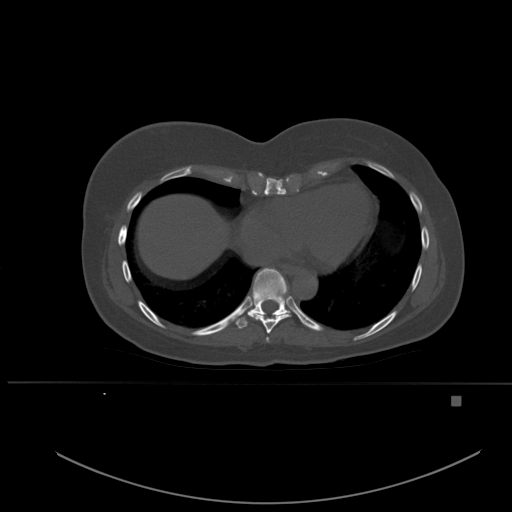
CT including the spine, one axial slice. Slice 313 of 651 in the series (ordered by position). Bone window (W 1800 / L 400 HU). 1.5 mm slice thickness. 512 × 512 image matrix, field of view 443 × 443 mm. Female patient, age 49 years. Case-level facts recorded for this patient, not image findings: primary cancer: breast; vertebrae with lytic lesions (as recorded): L3, T12, L4.
Annotated regions visible in this slice (semi-automatic segmentation, software-assisted and operator-edited):
- T7 vertebra: box from (x=266, y=337) to (x=269, y=342) px
- T8 vertebra: (x=247, y=312)–(x=291, y=334)
- T9 vertebra: (x=227, y=268)–(x=290, y=329)